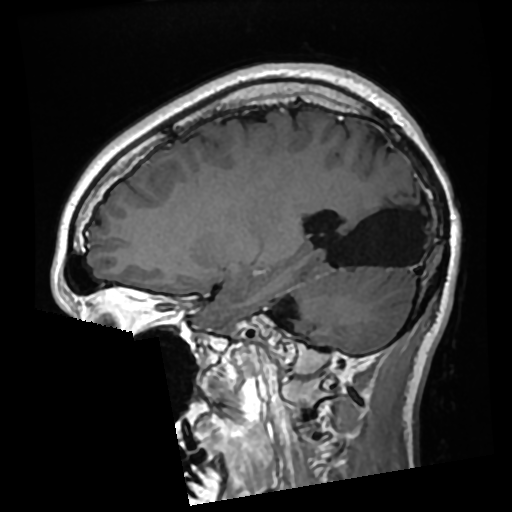
Brain MRI from a brain-tumour surgery series, one sagittal slice; T1-weighted post-contrast; 512 × 512 image matrix. From the clinical record (not read from this slice): histopathology: Glioma with ependymal features; WHO grade: 2; tumour location: Left Parietal.
Outlined on this slice (expert manual segmentation):
- previous resection cavity: bounding box [x1, y1, x2, y2] px = [327, 184, 424, 266]